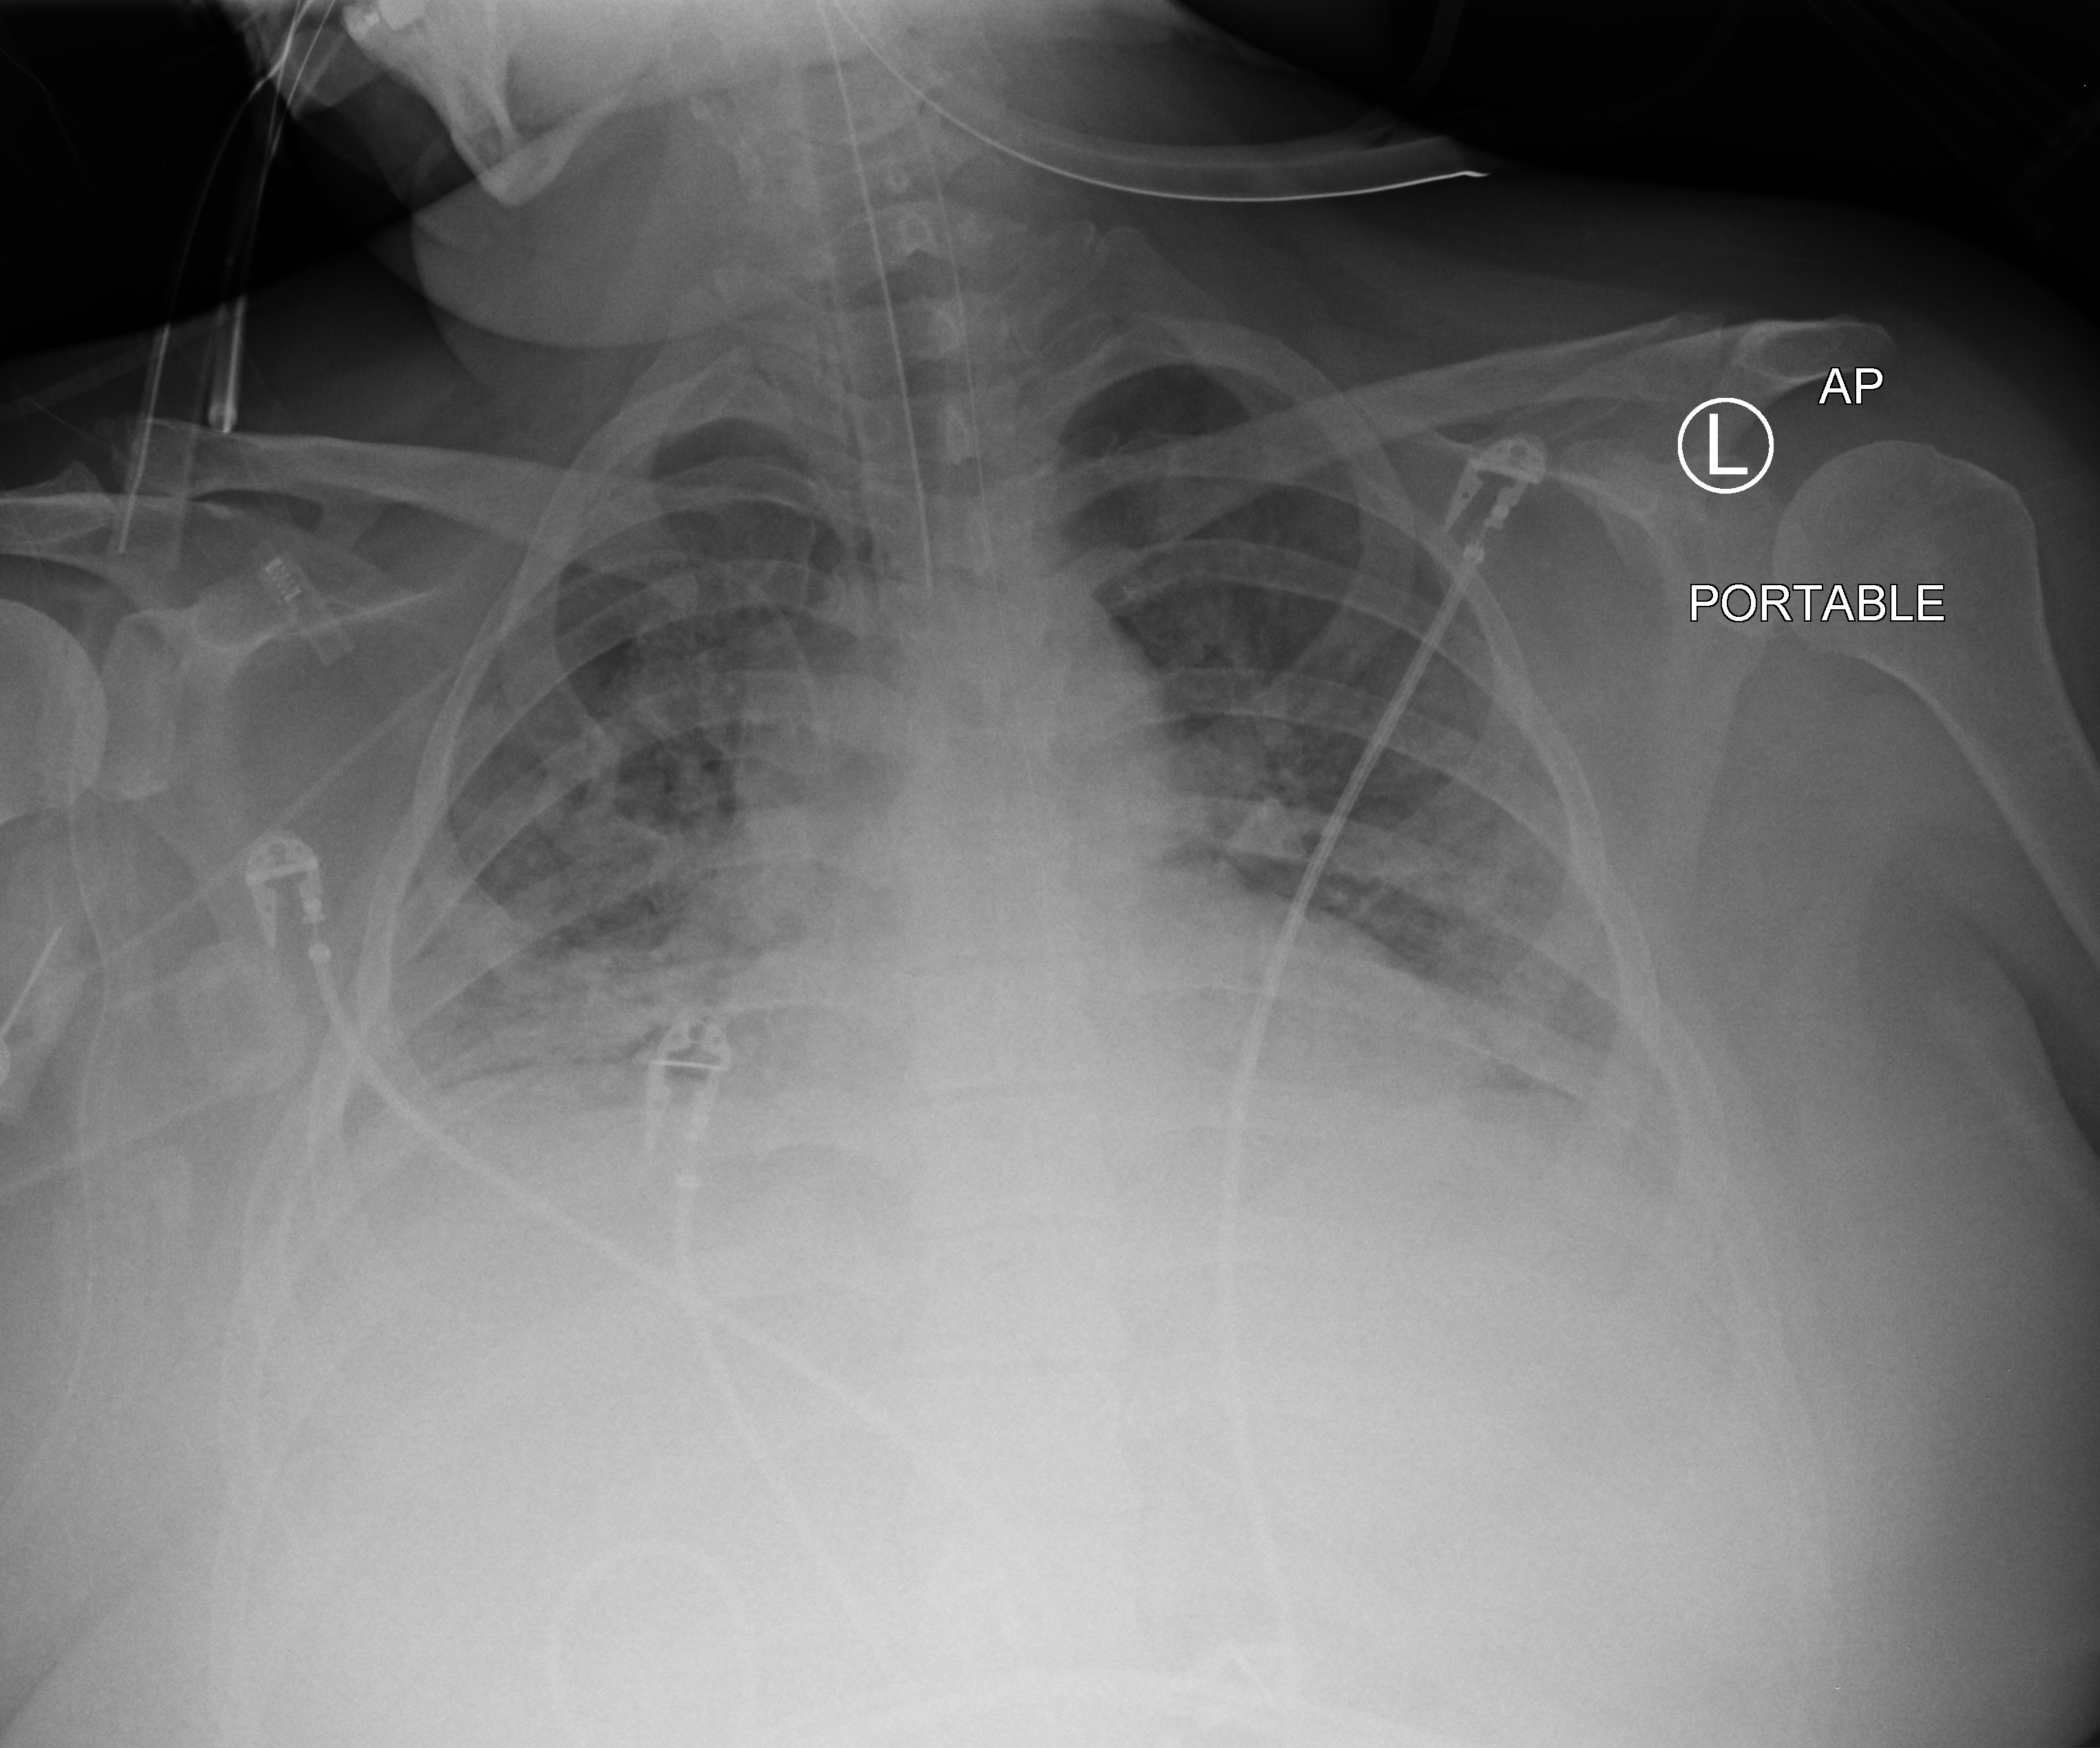
Portable chest radiograph. Patient hospitalised with COVID-19; female, aged 18–59 years.
Admission-level facts for this patient (not findings on this image; timing relative to this image not recorded):
- other chronic lung disease (admission record): no
- length of hospital stay: 25 days
- diabetes (admission record): no